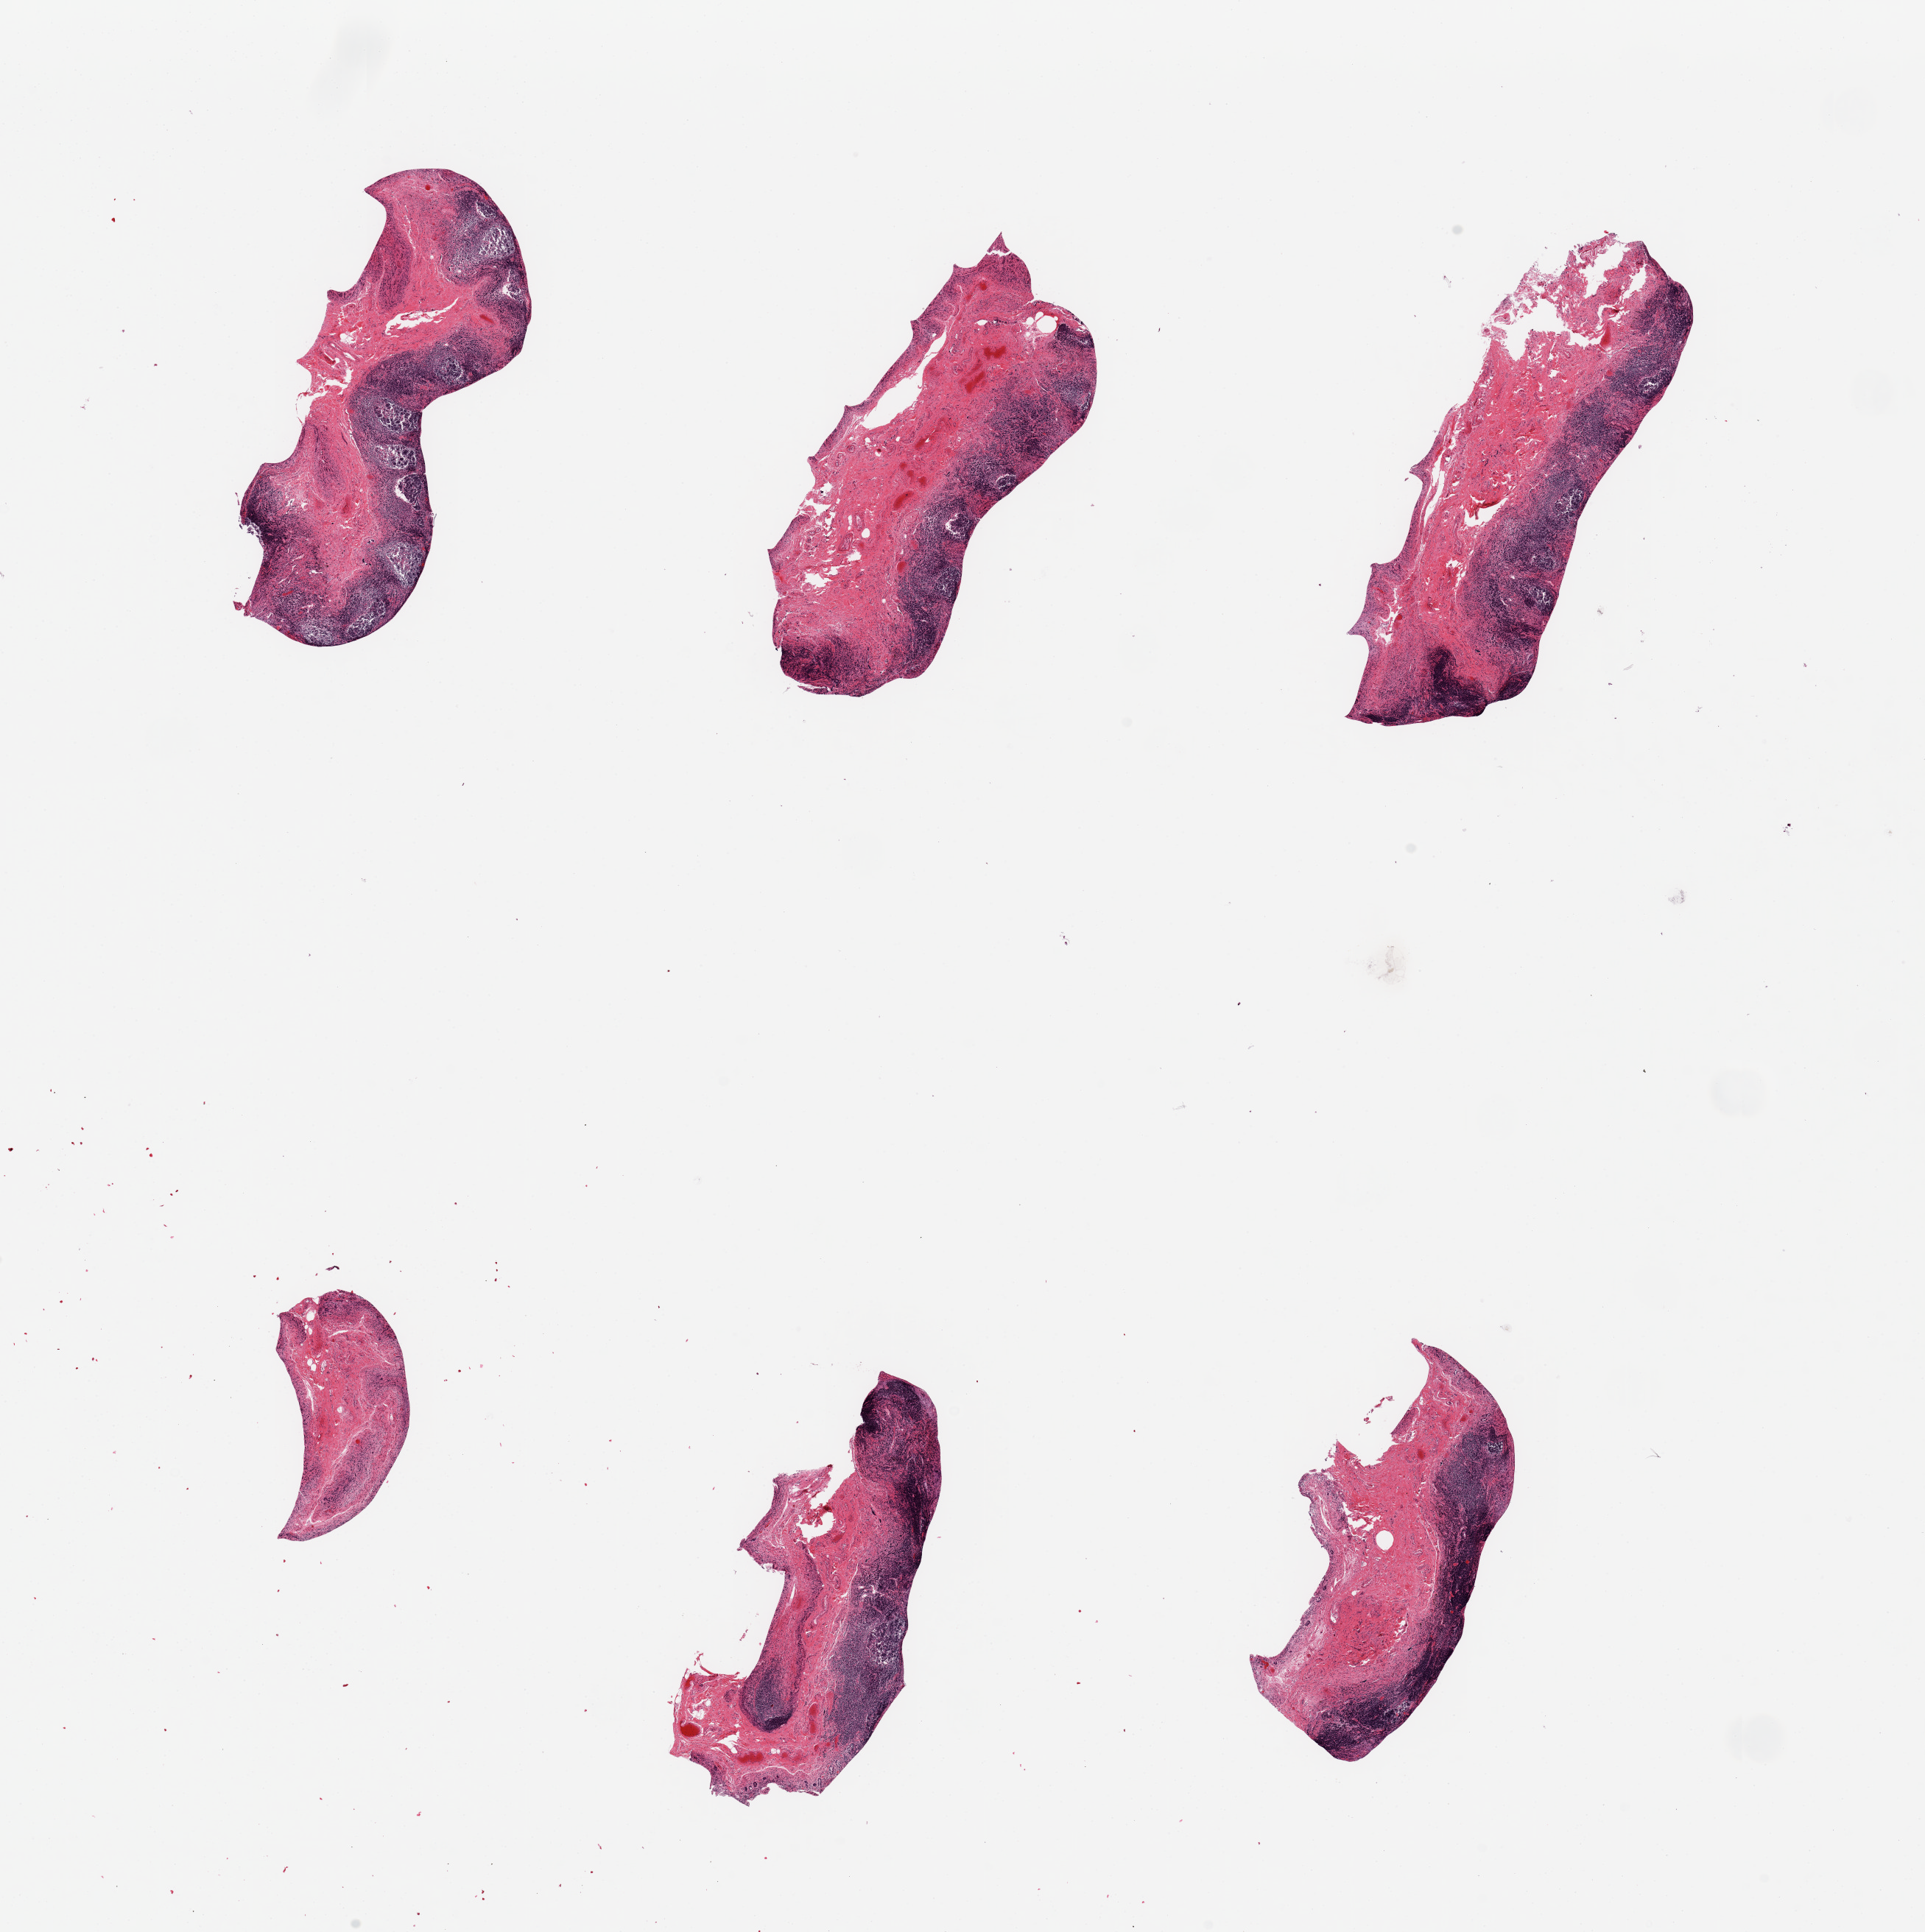
Digitized haematoxylin and eosin-stained section, brightfield, shown as a low-resolution overview of the whole scanned area (about 20.7 x 20.8 mm). PAXgene-fixed, paraffin-embedded tissue. Target tissue: ileum. Donor tissue sample. Male donor.
• pathologist's review note for this sample: 6 pieces ~5x1.5mm. Includes muscle and lymphoid aggregates, epithelium autolyzed and sloughed. ~50% of specimen are lymphocytes